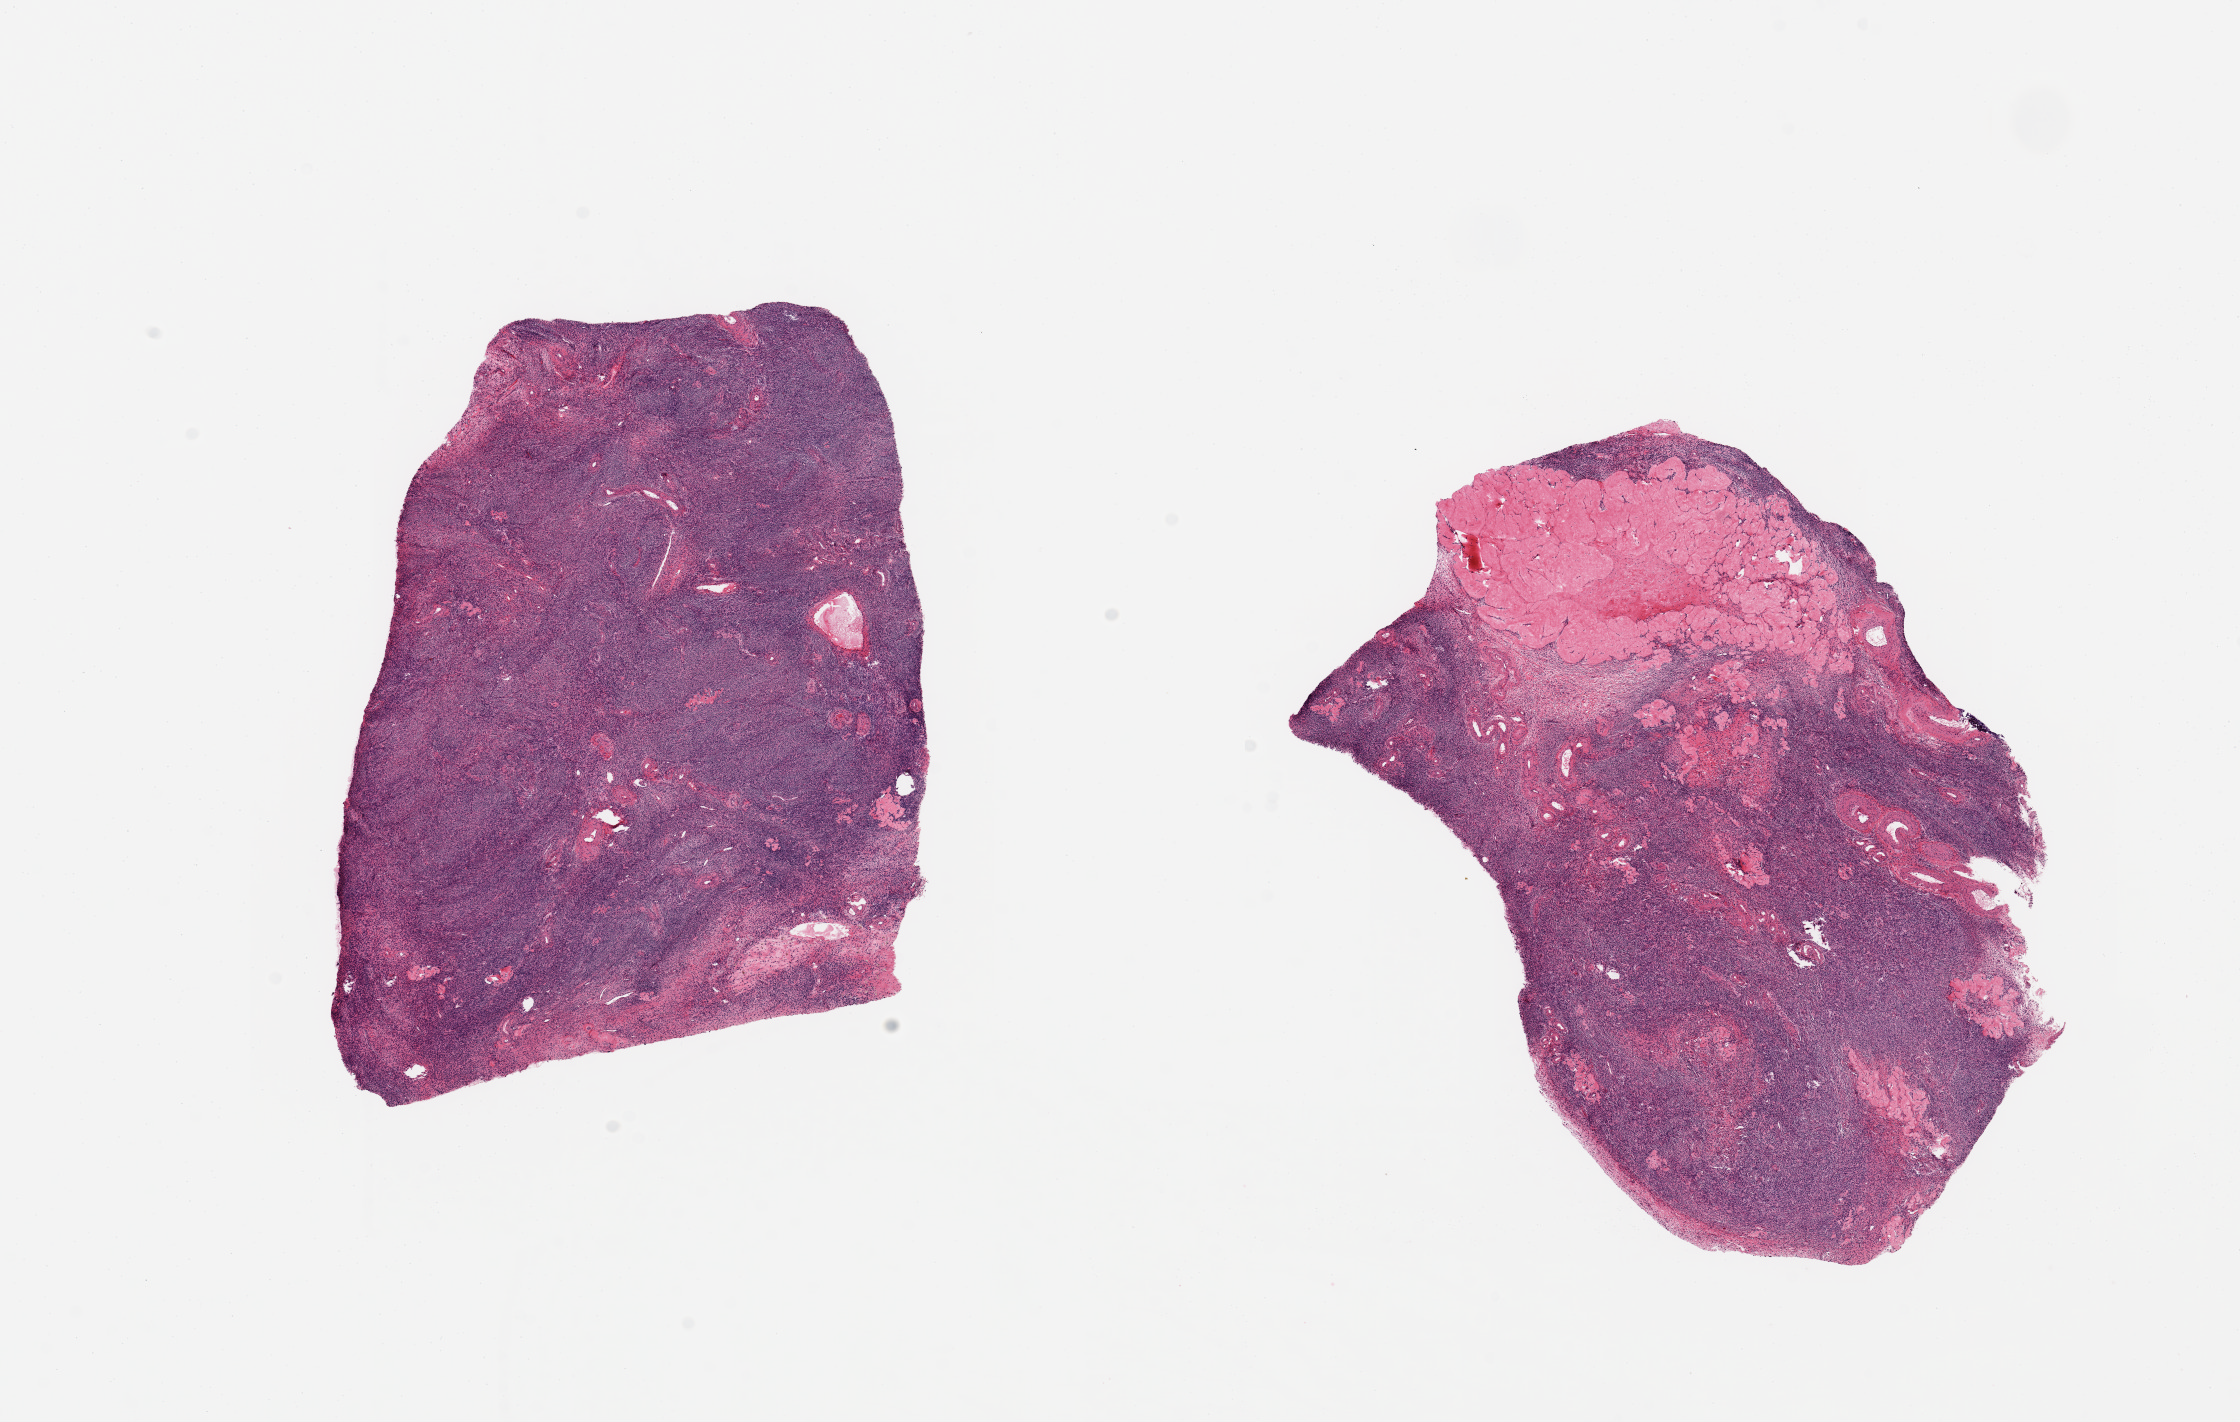
Digitized H&E-stained section, a low-resolution overview of the entire scanned area, about 17.7 x 11.2 mm. PAXgene-fixed, paraffin-embedded tissue. Section of ovary (target tissue). Tissue donor sample.
* review note (as recorded): 2 ~6.6x4.3mm pieces, post-menopausal stroma